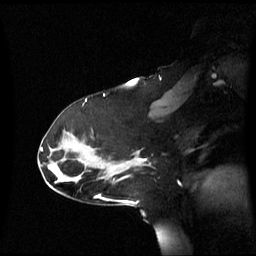
Breast MRI (dynamic contrast-enhanced), one sagittal slice; position 38 of 60 along the scan axis; dynamic contrast-enhanced series, image 2 of 3 at this slice position (ordered by acquisition); 1.5 T; TE 4.2 ms, TR 8.4 ms; 256 × 256 image matrix, field of view 270 × 270 mm. Patient: female, 39 years. From the clinical record (not read from this slice): setting: breast cancer imaged before/during neoadjuvant chemotherapy; receptor status: triple-negative.
Annotated regions visible in this slice (semi-automatically segmented with operator editing):
- analysis volume of interest (the breast-tissue region the enhancement analysis was run in; not a lesion): bounding box [x1, y1, x2, y2] px = [117, 151, 150, 174]
- tumour enhancement mask (voxels above the 70 % enhancement threshold inside the analysis volume of interest): [138, 158, 147, 162]